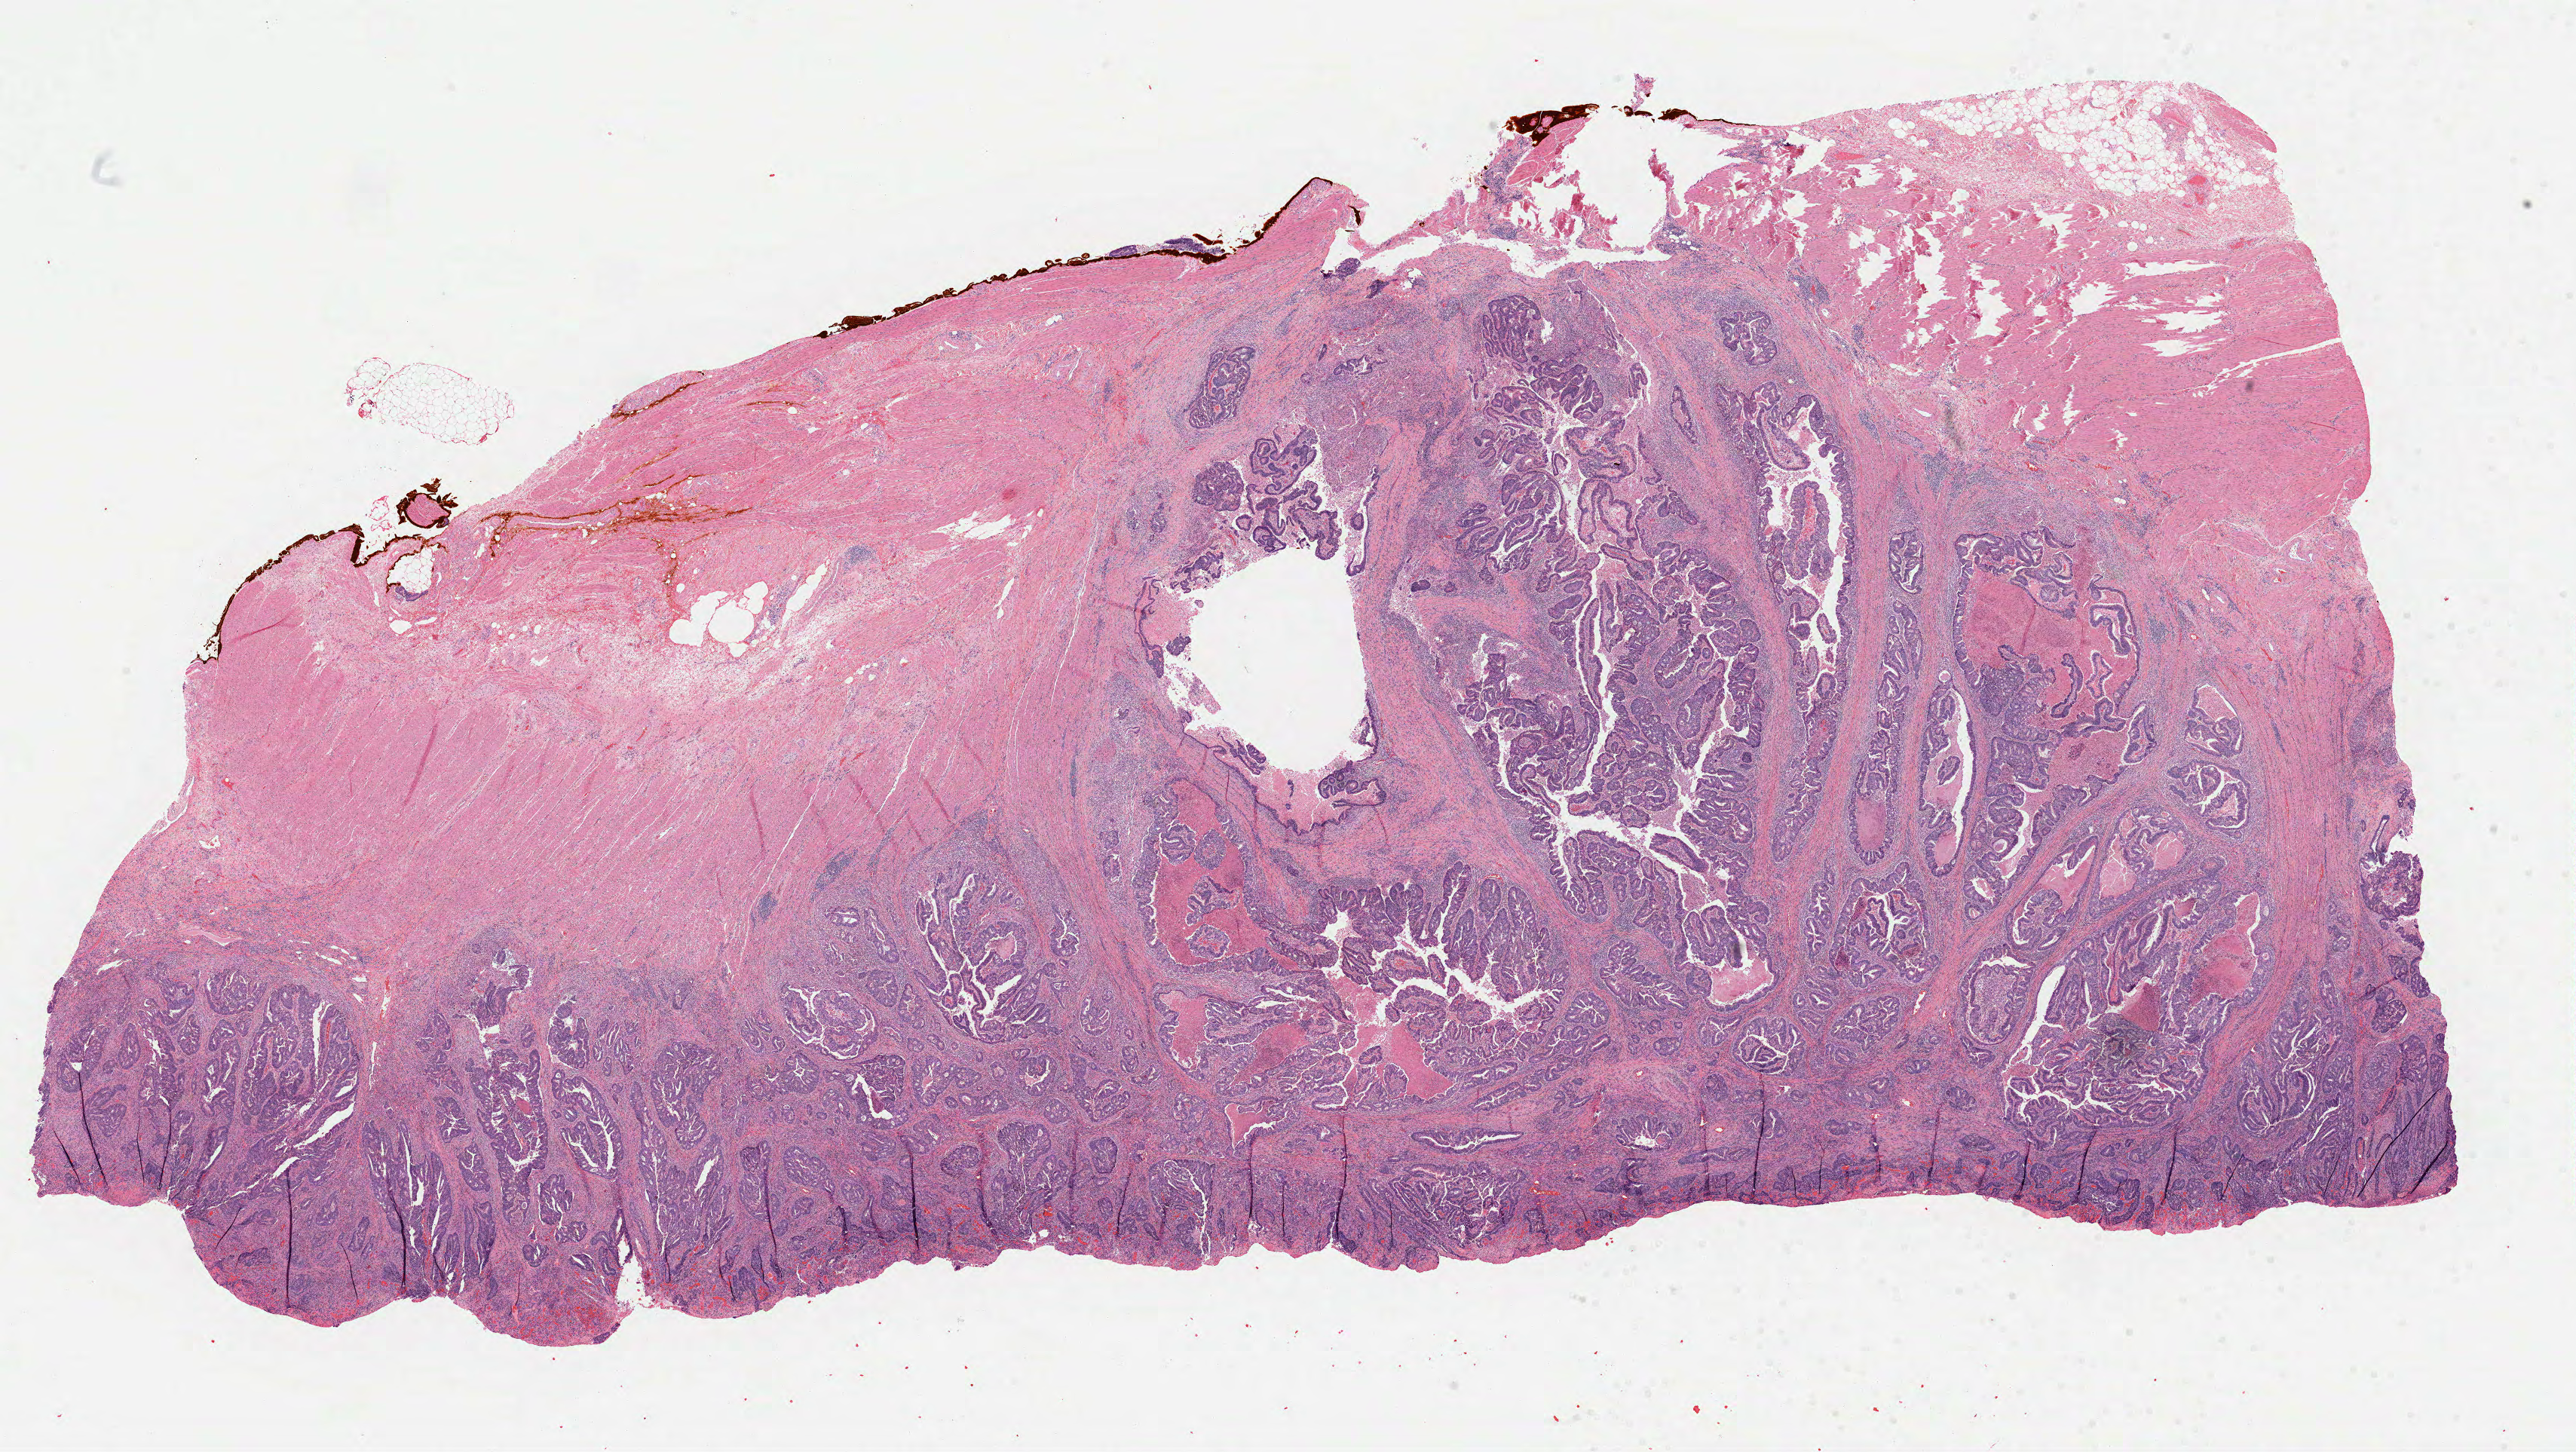
Digitized H&E tissue section (whole slide) — low-resolution overview of the scanned area, about 27.6 x 15.5 mm (from a 40x scan), formalin-fixed paraffin-embedded (FFPE) diagnostic section, primary tumour sample from the rectum. Patient sex: female.
AJCC pathologic stage: IIA. TNM: T3 N0 MX. Pathologic diagnosis: Adenocarcinoma, NOS.